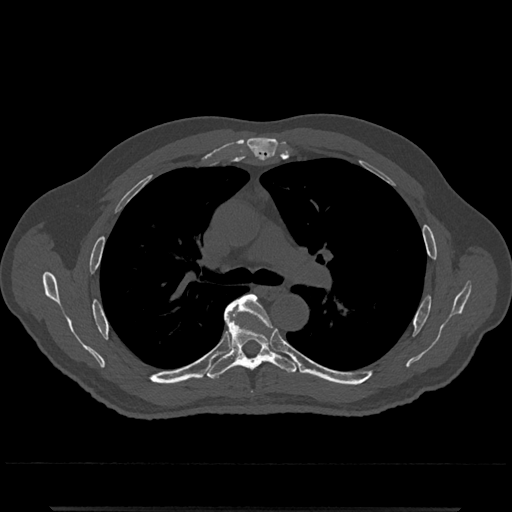
CT including the spine, one axial slice; slice 790 of 797 in the series (ordered by position); 120 kVp; bone window (W 1800 / L 400 HU); 512 × 512 image matrix, field of view 393 × 393 mm. Patient: male, 67 years. From the clinical record (not read from this slice): primary cancer: prostate.
Annotated regions visible in this slice (semi-automatic segmentation, software-assisted and operator-edited):
- T5 vertebra: bounding box [x1, y1, x2, y2] px = [227, 294, 269, 320]
- T6 vertebra: [205, 301, 298, 380]